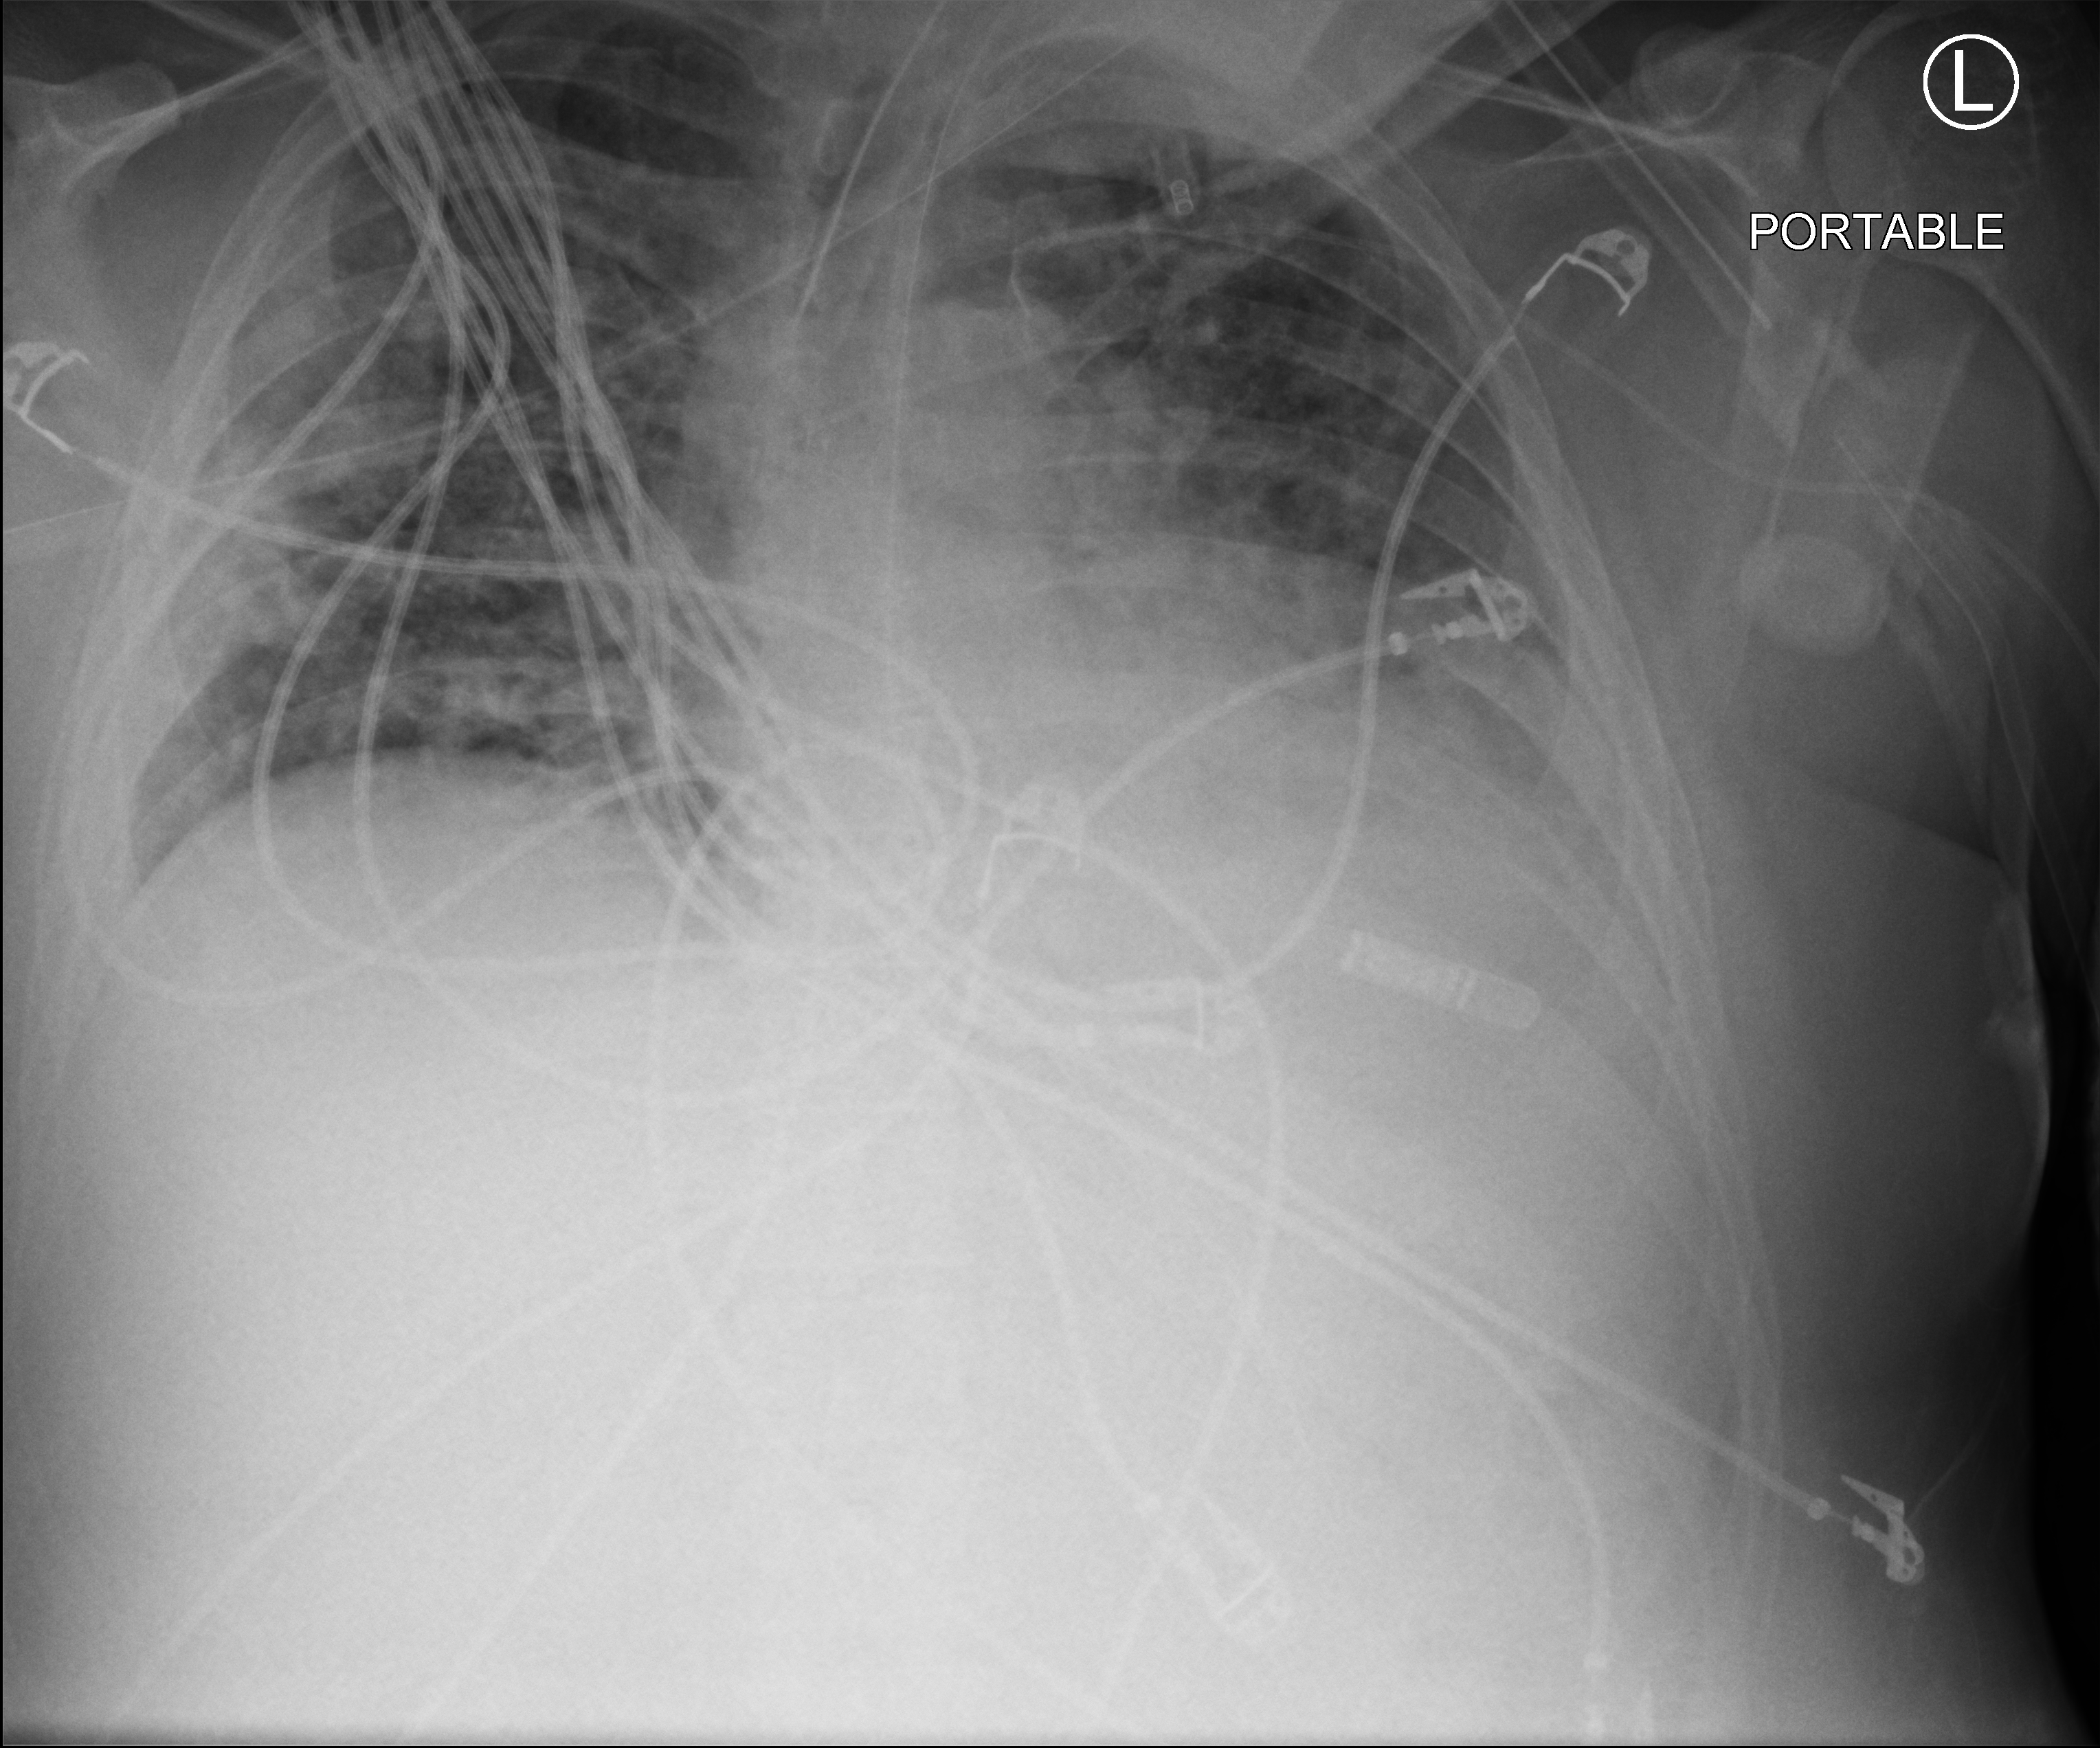
Portable chest radiograph. Male patient hospitalised with COVID-19, age 18–59 years.
From the hospital-stay record, not from the radiograph (when in the stay this image was taken is not recorded): length of hospital stay: 39 days; mechanically ventilated during this hospital stay: yes; admitted to intensive care during this hospital stay: yes.